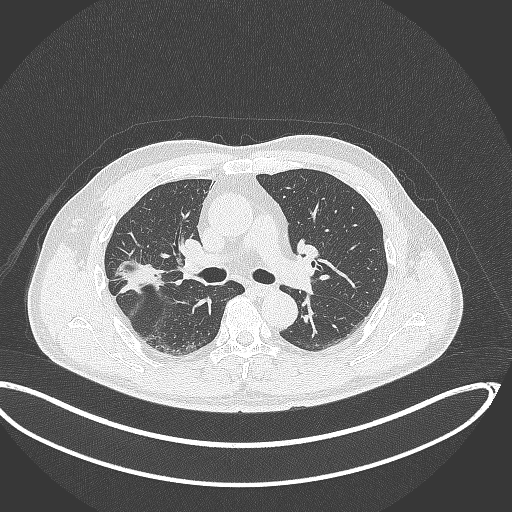
Chest CT, one axial slice; slice 207 of 391 in the series (ordered by position); 120 kVp; lung window (W 1500 / L -600 HU); 1 mm slice thickness; 512 × 512 image matrix. Patient: male, 63 years. From the clinical record (not read from this slice): clinical TNM (as recorded): T1c N0 M0; histopathological grade: G2-3.
Structures marked on this image (rectangle marked by the reading radiologist):
- lung tumour (recorded histology: adenocarcinoma): bounding box (x1, y1, x2, y2) in pixels: (114, 255, 166, 302)